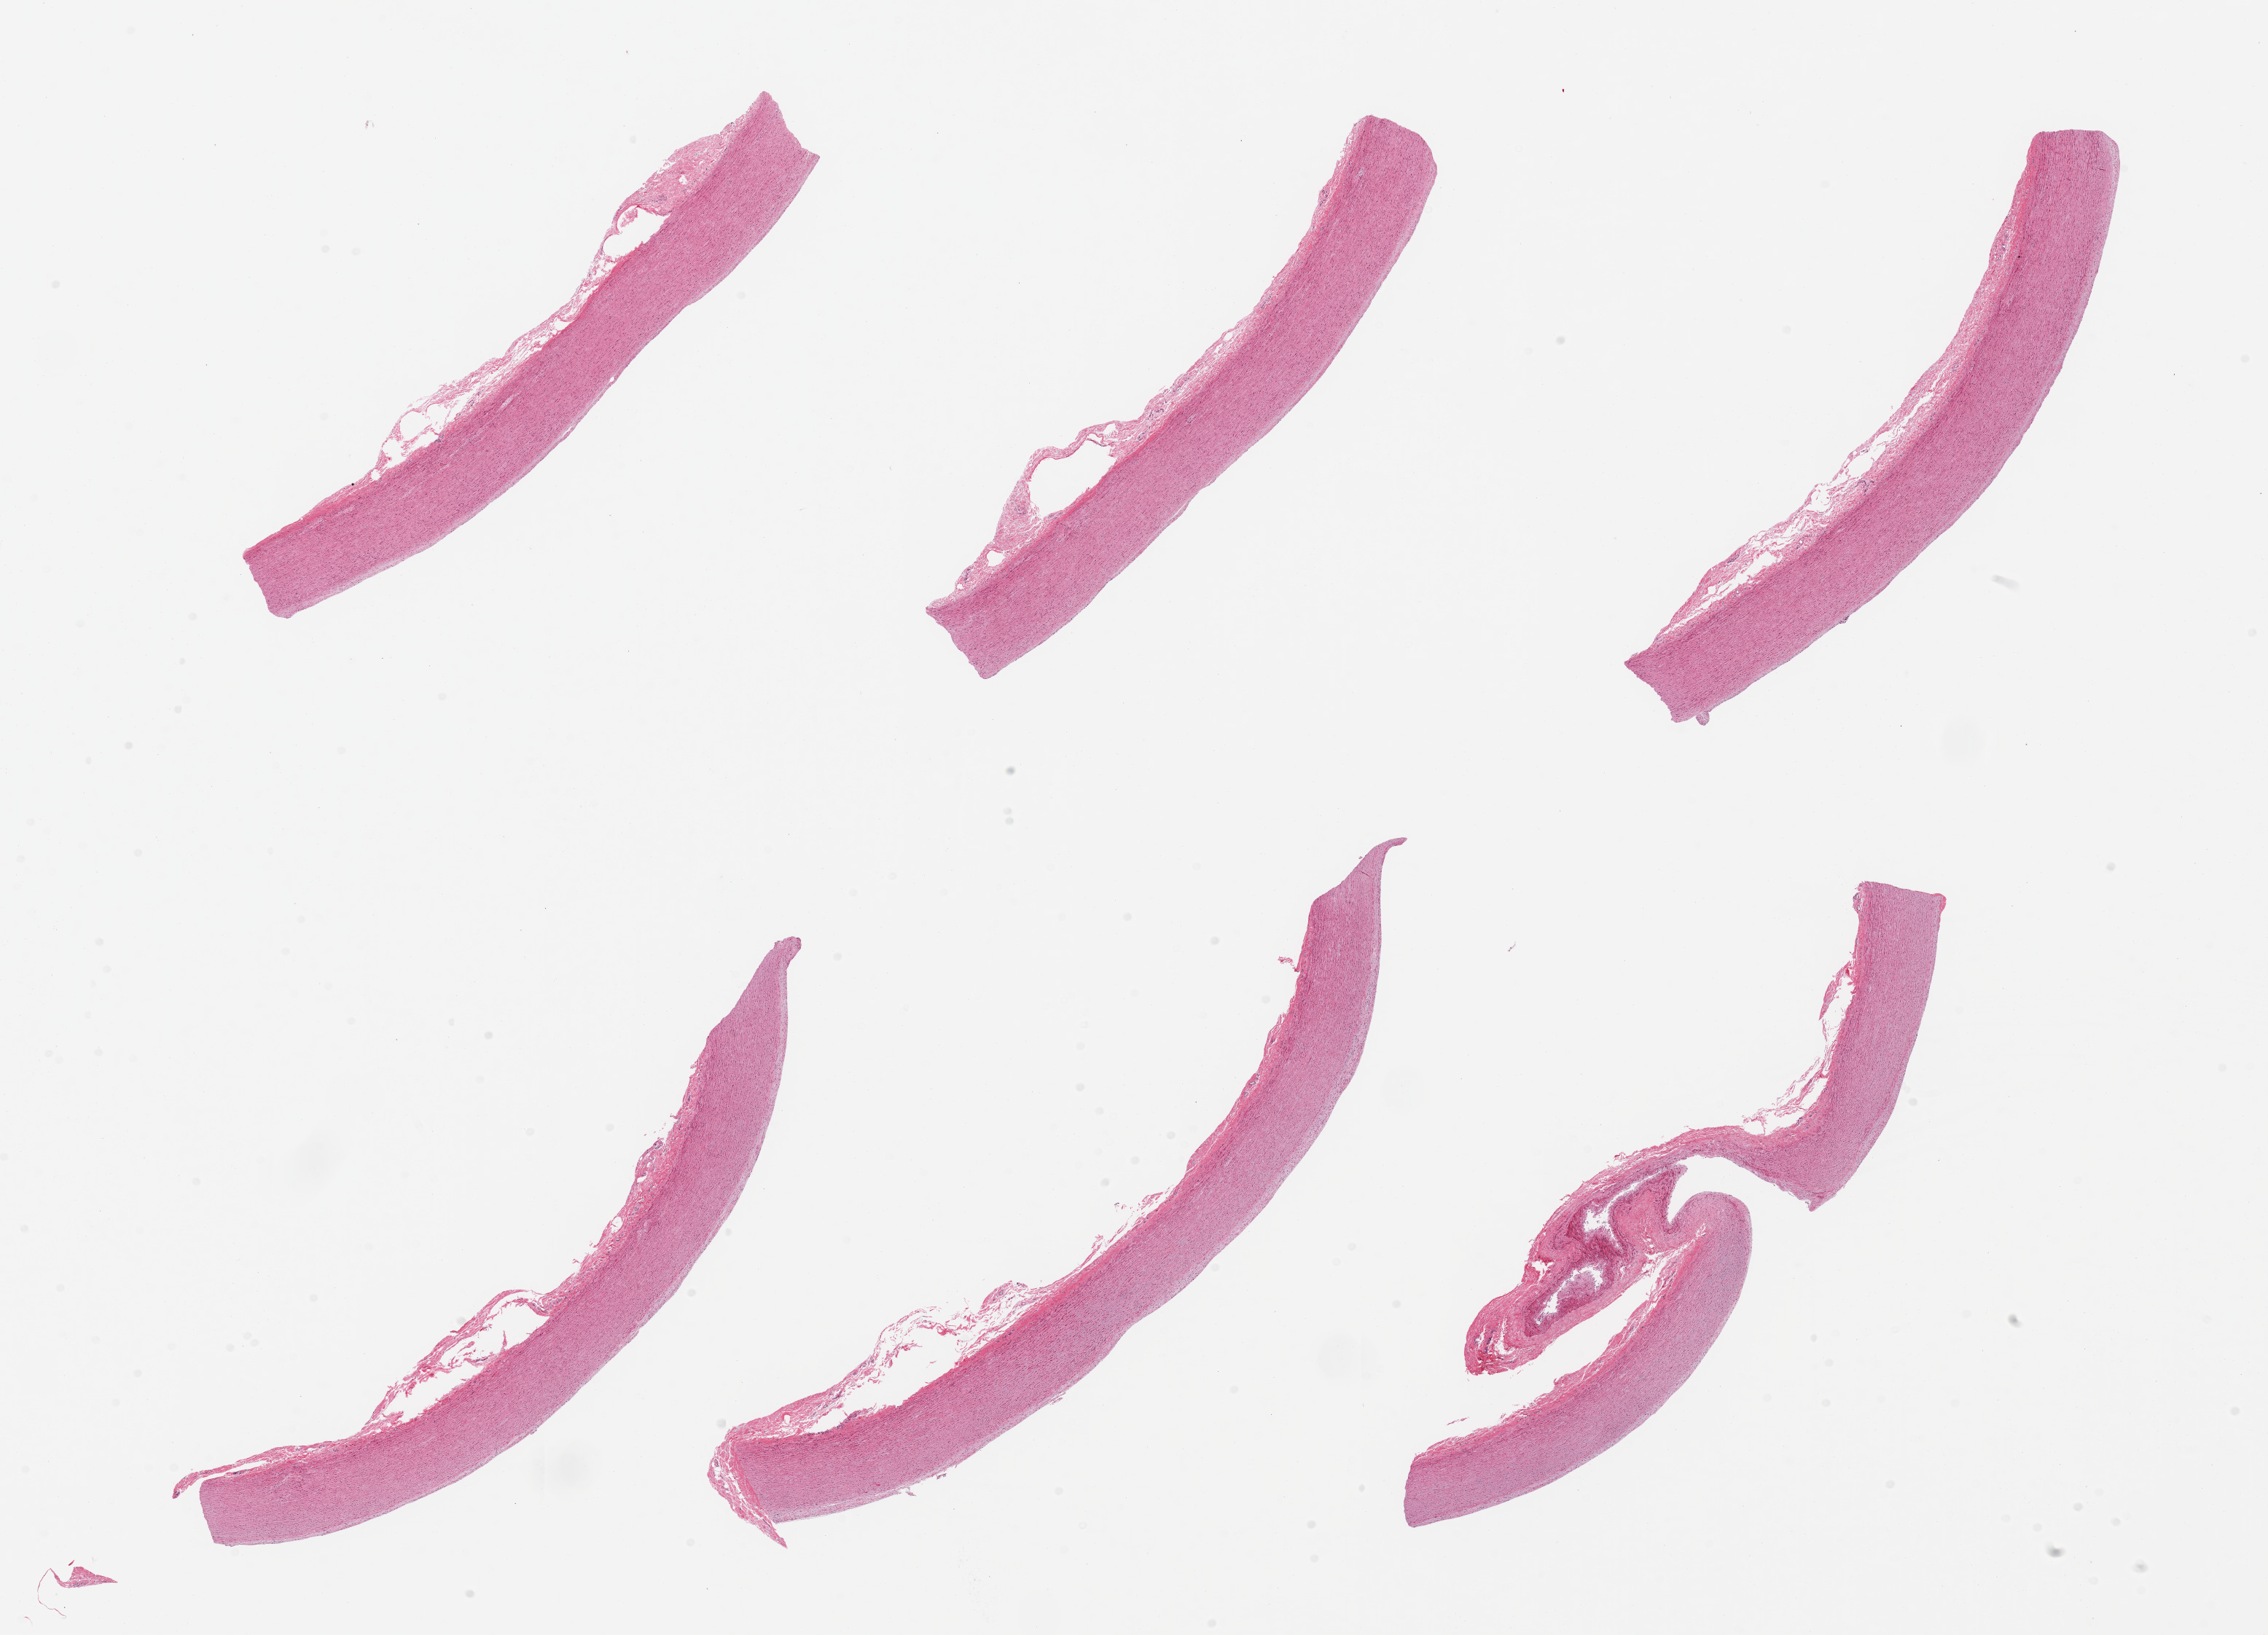
Digitized haematoxylin and eosin-stained section — low-resolution overview of the scanned area, about 24.6 x 17.7 mm, PAXgene-fixed, paraffin-embedded tissue, section of aorta (target tissue), tissue donor sample. Female donor.
Reviewer comment on this tissue sample: 6 pieces, trace atherosis, <0.1mm.